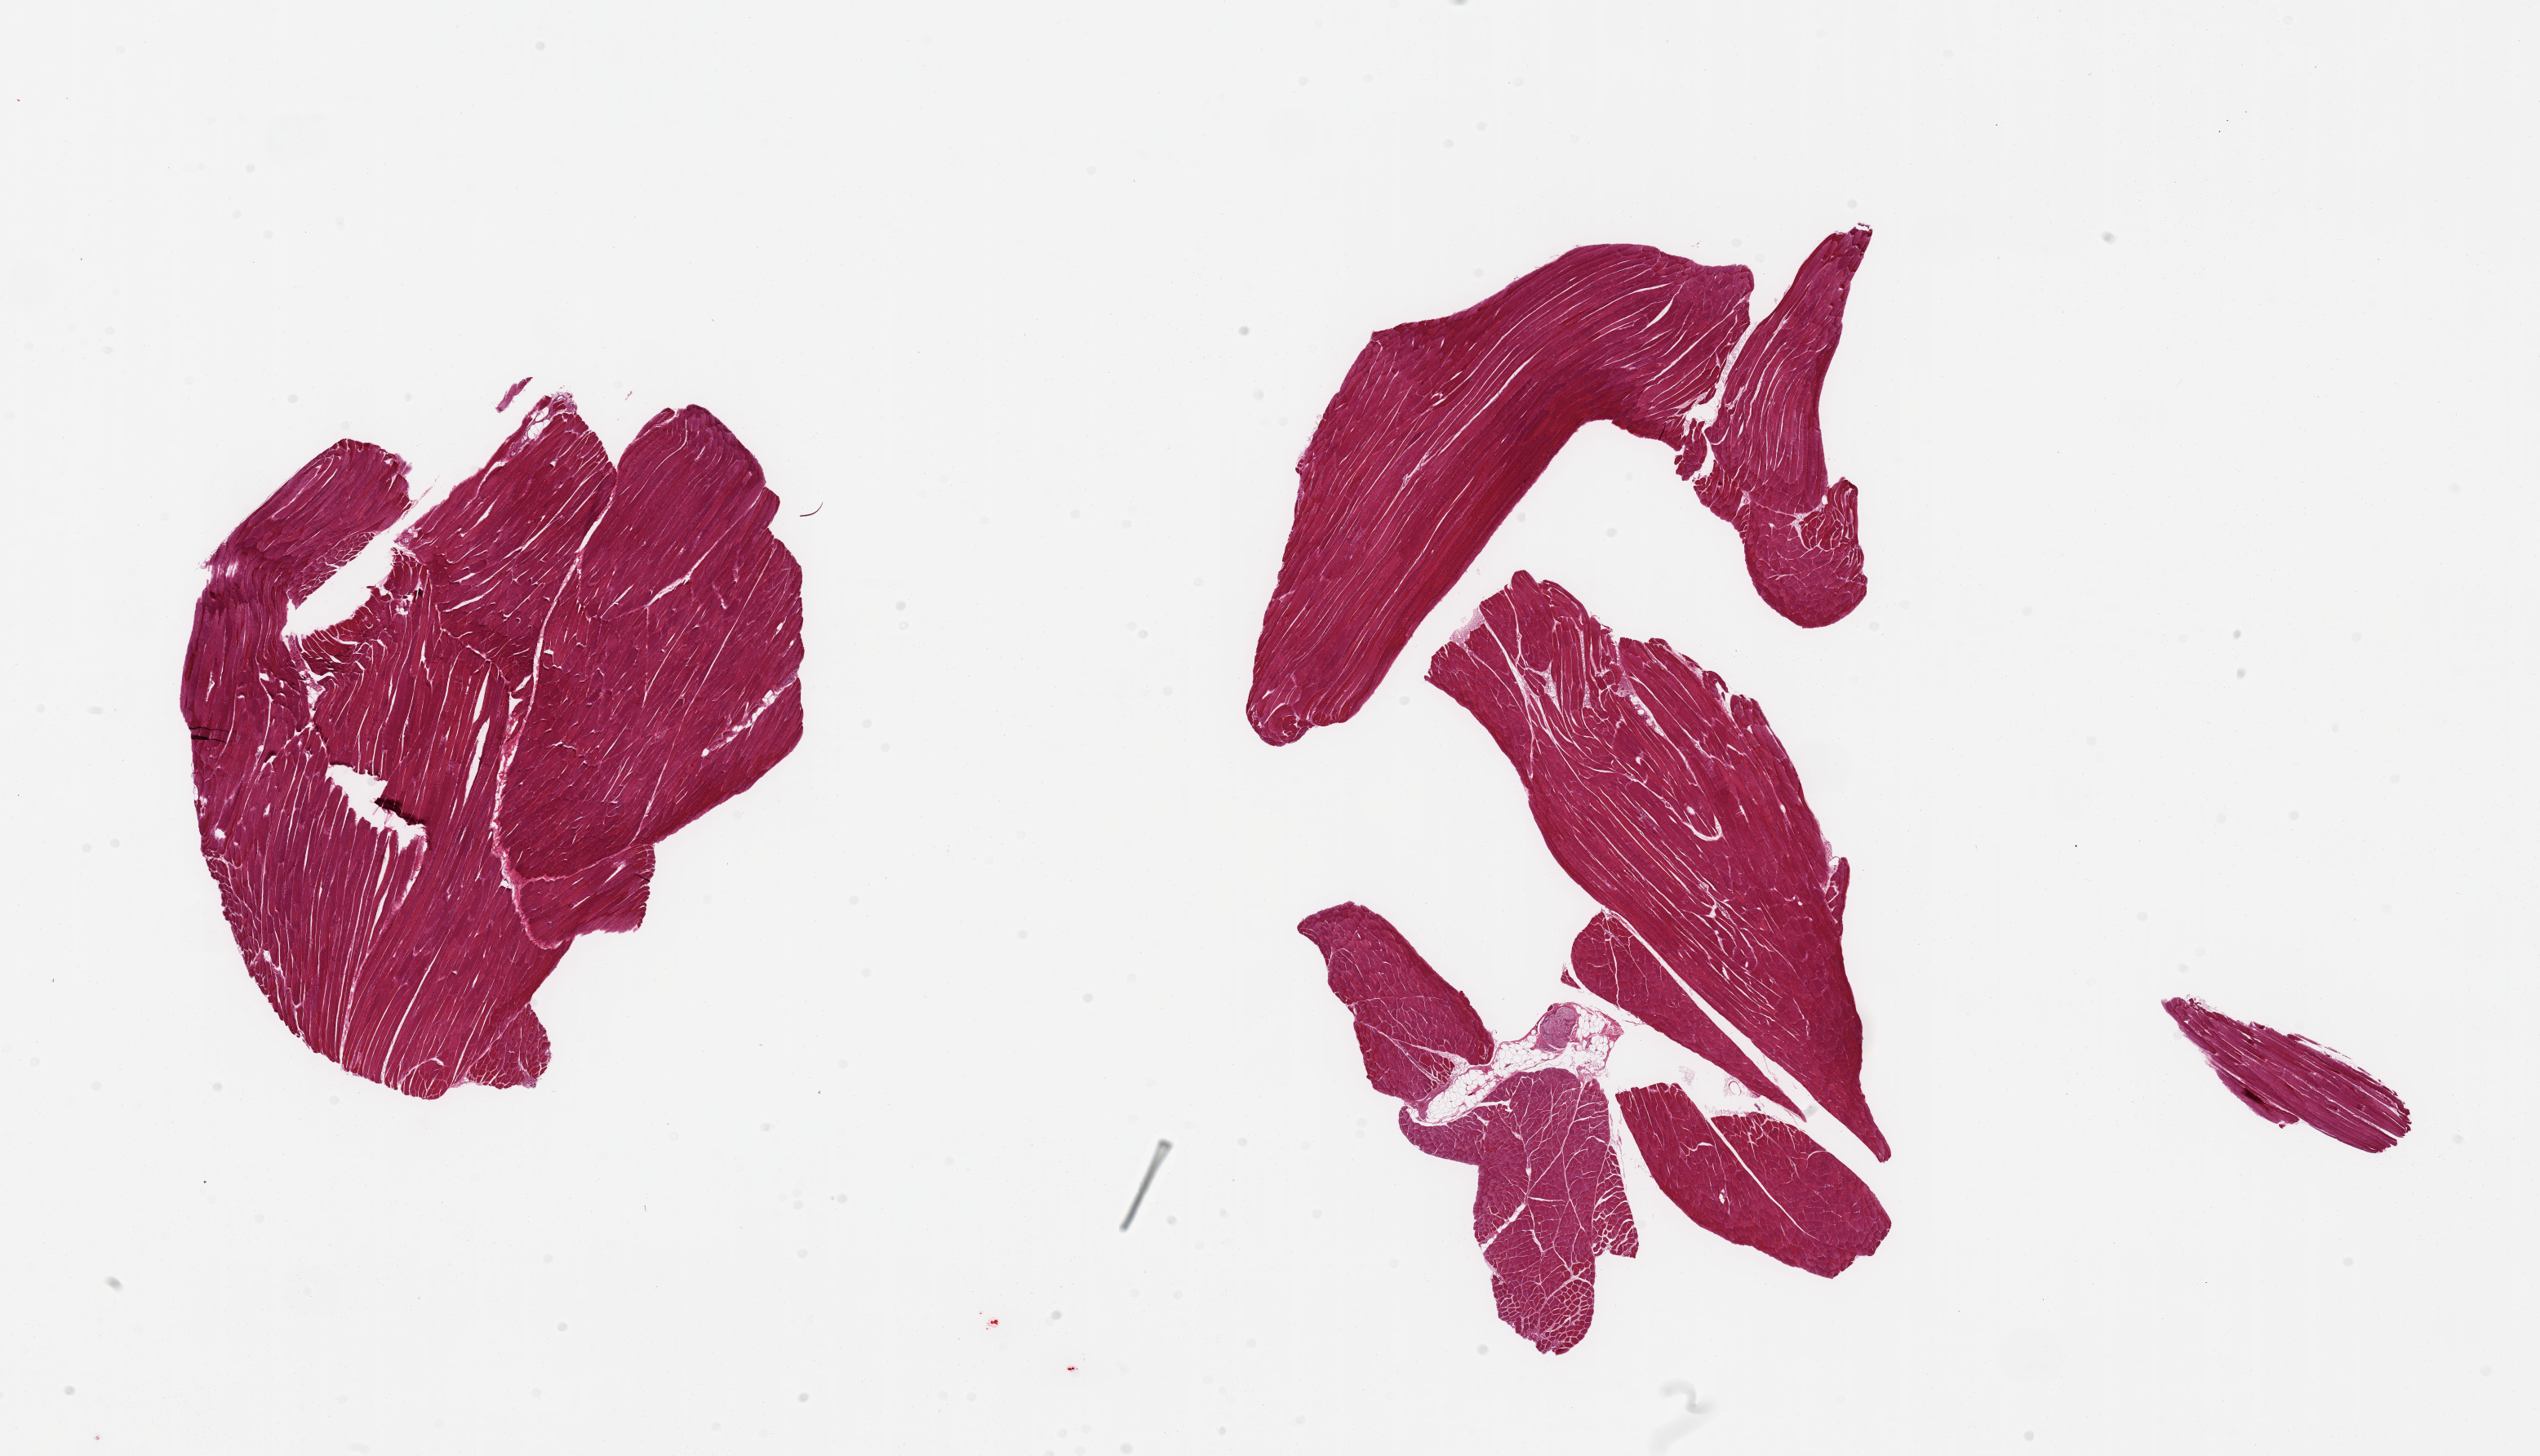
Haematoxylin and eosin whole-slide image, brightfield — shown as a low-resolution overview of the whole scanned area (about 24.6 x 14.1 mm). PAXgene-fixed paraffin-embedded (PFPE) section. Section of skeletal muscle (target tissue). Tissue donor sample. Donor: male.
Reviewer comment on this tissue sample: 2 pieces, interstitial fat/neural elements are ~5% of tissue.